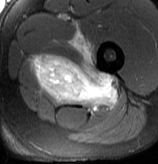
MRI of an extremity soft-tissue mass, one axial slice; slice 58 of 70 in the series (ordered by position); T2-weighted fat-saturated; MR volume resampled by the dataset authors to the PET/CT grid (not the native acquisition matrix); 3.27 mm slice thickness; 158 × 164 image matrix, field of view 154 × 160 mm. Male patient. From the clinical record (not read from this slice): histological type: extraskeletal osteosarcoma; grade: high; site of the primary tumour: left adductur.
Structures marked on this image (expert contour drawn on MRI and transferred to this co-registered scan by the dataset authors):
- gross tumour volume (mass): bounding box <29,30,119,108> (left, top, right, bottom; pixels)